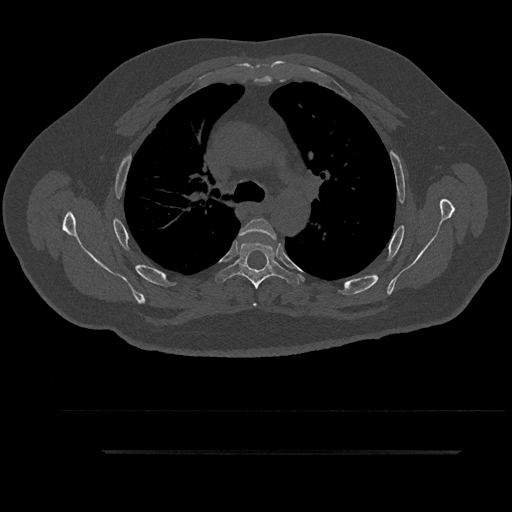
CT including the spine, one axial slice; slice 639 of 797 in the series (ordered by position); 120 kVp; bone window (W 1800 / L 400 HU); 0.5 mm slice thickness; 512 × 512 image matrix, field of view 432 × 432 mm. Patient: male, 63 years. From the clinical record (not read from this slice): primary cancer: renal; vertebrae with lytic lesions (as recorded): T8.
Outlined on this slice (semi-automatic segmentation, software-assisted and operator-edited):
- T4 vertebra: bounding box <238,218,278,306> (left, top, right, bottom; pixels)
- T5 vertebra: <215,241,299,289>